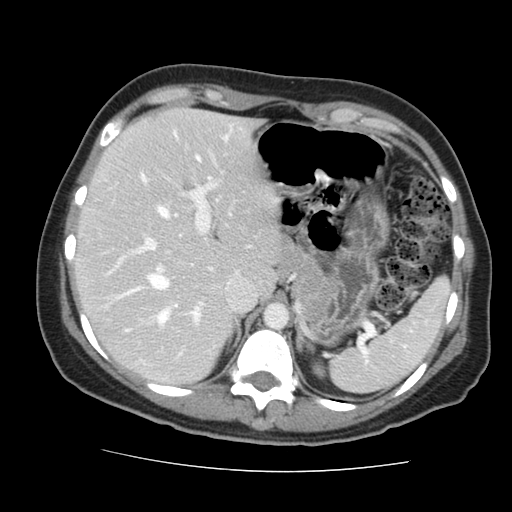
Contrast-enhanced abdominal CT, one axial slice. Position 105 of 144 along the scan axis. 120 kVp. Intravenous contrast given. Soft-tissue window (W 400 / L 40 HU). 2.5 mm slice thickness. 512 × 512 image matrix, field of view 333 × 333 mm. Female patient, age 46 years. Case-level facts recorded for this patient, not image findings: diagnosis: colorectal cancer liver metastases, imaged before liver resection; multiple liver metastases: no; largest metastasis: 2.8 cm; disease in both lobes: no.
Outlined on this slice (outlined manually by an expert reader):
- hepatic veins: box from (x=126, y=175) to (x=177, y=318) px
- liver: (x=78, y=109)–(x=276, y=383)
- planned liver remnant (the part of the liver to remain after resection): (x=78, y=109)–(x=276, y=383)
- portal vein (with intrahepatic branches): (x=109, y=182)–(x=232, y=332)